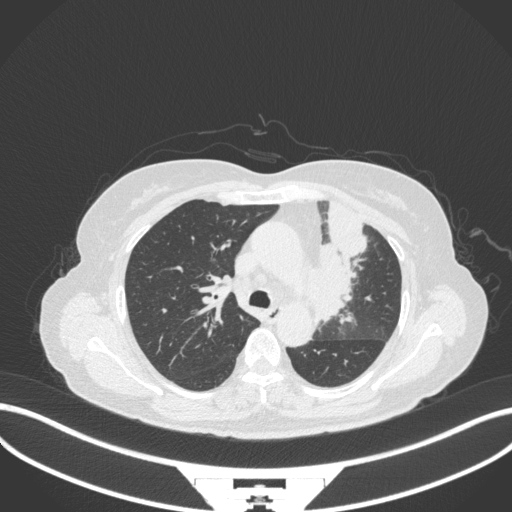
Chest CT, one axial slice. Slice 227 of 382 in the series (ordered by position). Reconstruction kernel B31f. Lung window (W 1500 / L -600 HU). 1 mm slice thickness. 512 × 512 image matrix. Female patient, age 64 years. From the clinical record (not read from this slice): clinical TNM (as recorded): T2a N2 M0.
Annotated regions visible in this slice (rectangle marked by the reading radiologist):
- lung tumour (recorded histology: adenocarcinoma): bounding box <304,196,368,323> (left, top, right, bottom; pixels)